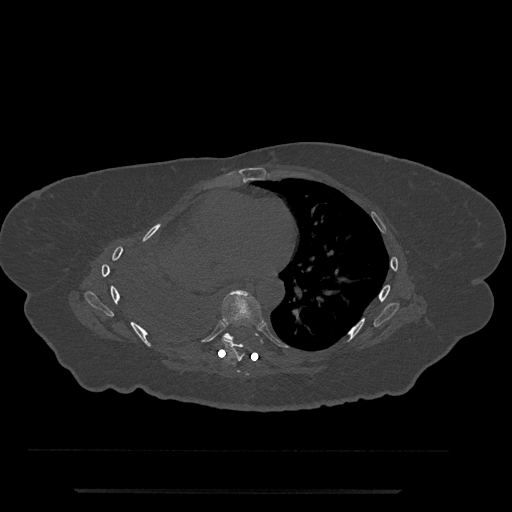
CT including the spine, one axial slice; position 427 of 797 along the scan axis; 120 kVp; bone window (W 1800 / L 400 HU); 0.5 mm slice thickness; 512 × 512 image matrix. Patient: female, 51 years. Case-level facts recorded for this patient, not image findings: primary cancer: neuro; vertebrae with lytic lesions (as recorded): T8.
Structures marked on this image (semi-automatic segmentation, software-assisted and operator-edited):
- T6 vertebra: bounding box <237,370,240,373> (left, top, right, bottom; pixels)
- T7 vertebra: <221,290,263,362>
- T8 vertebra: <222,333,234,341>